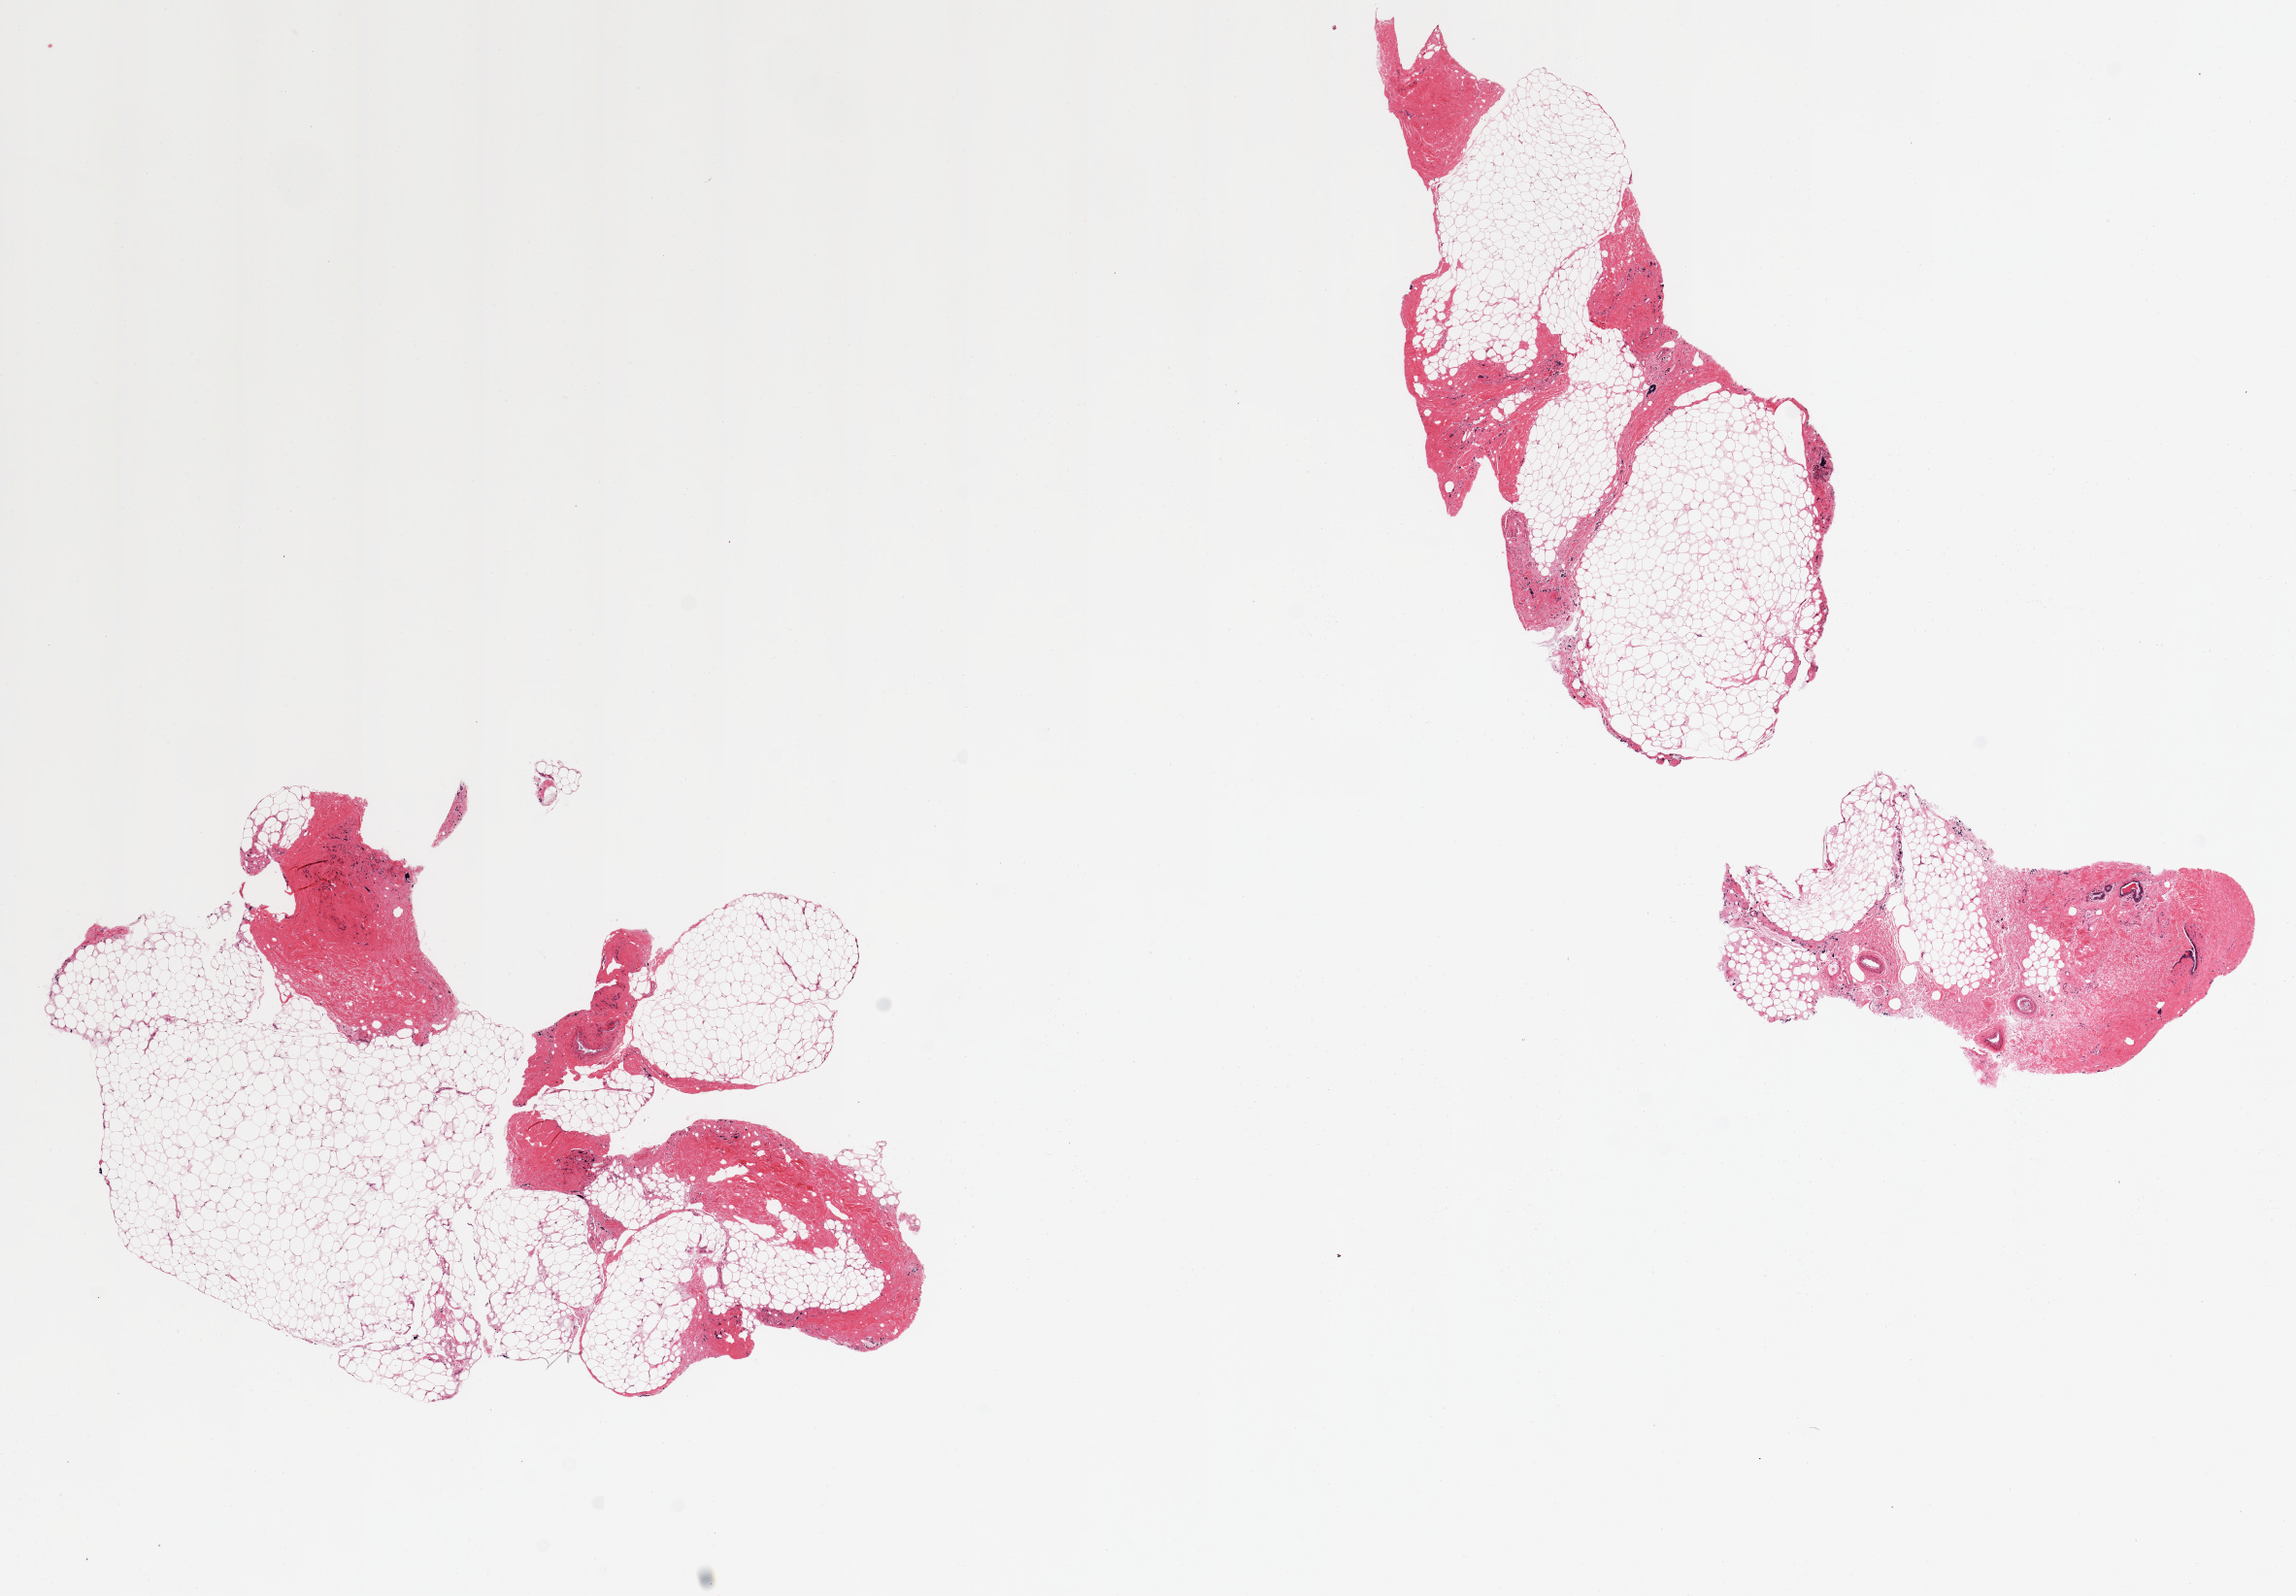
H&E whole-slide image — a low-resolution overview of the entire scanned area, about 18.7 x 13.0 mm; PAXgene-fixed, paraffin-embedded tissue; target tissue: breast; donor tissue sample. Male donor.
• review note (as recorded): 2 pieces; fibroadipose tissue with ducts